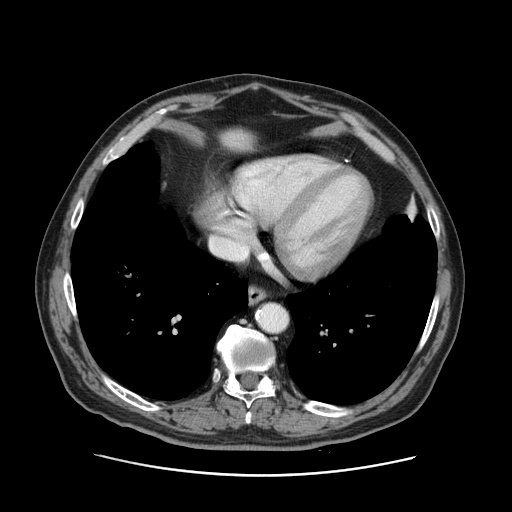
Contrast-enhanced abdominal CT, one axial slice. Slice 126 of 141 in the series (ordered by position). 120 kVp. Intravenous contrast given. Soft-tissue window (W 400 / L 40 HU). 512 × 512 image matrix, field of view 395 × 395 mm. Male patient, age 72 years. From the clinical record (not read from this slice): diagnosis: colorectal cancer liver metastases, imaged before liver resection; multiple liver metastases: yes; largest metastasis: 5.4 cm; disease in both lobes: yes.
Structures marked on this image (outlined manually by an expert reader):
- liver: bounding box [x1, y1, x2, y2] px = [222, 129, 254, 150]
- planned liver remnant (the part of the liver to remain after resection): [222, 129, 256, 150]